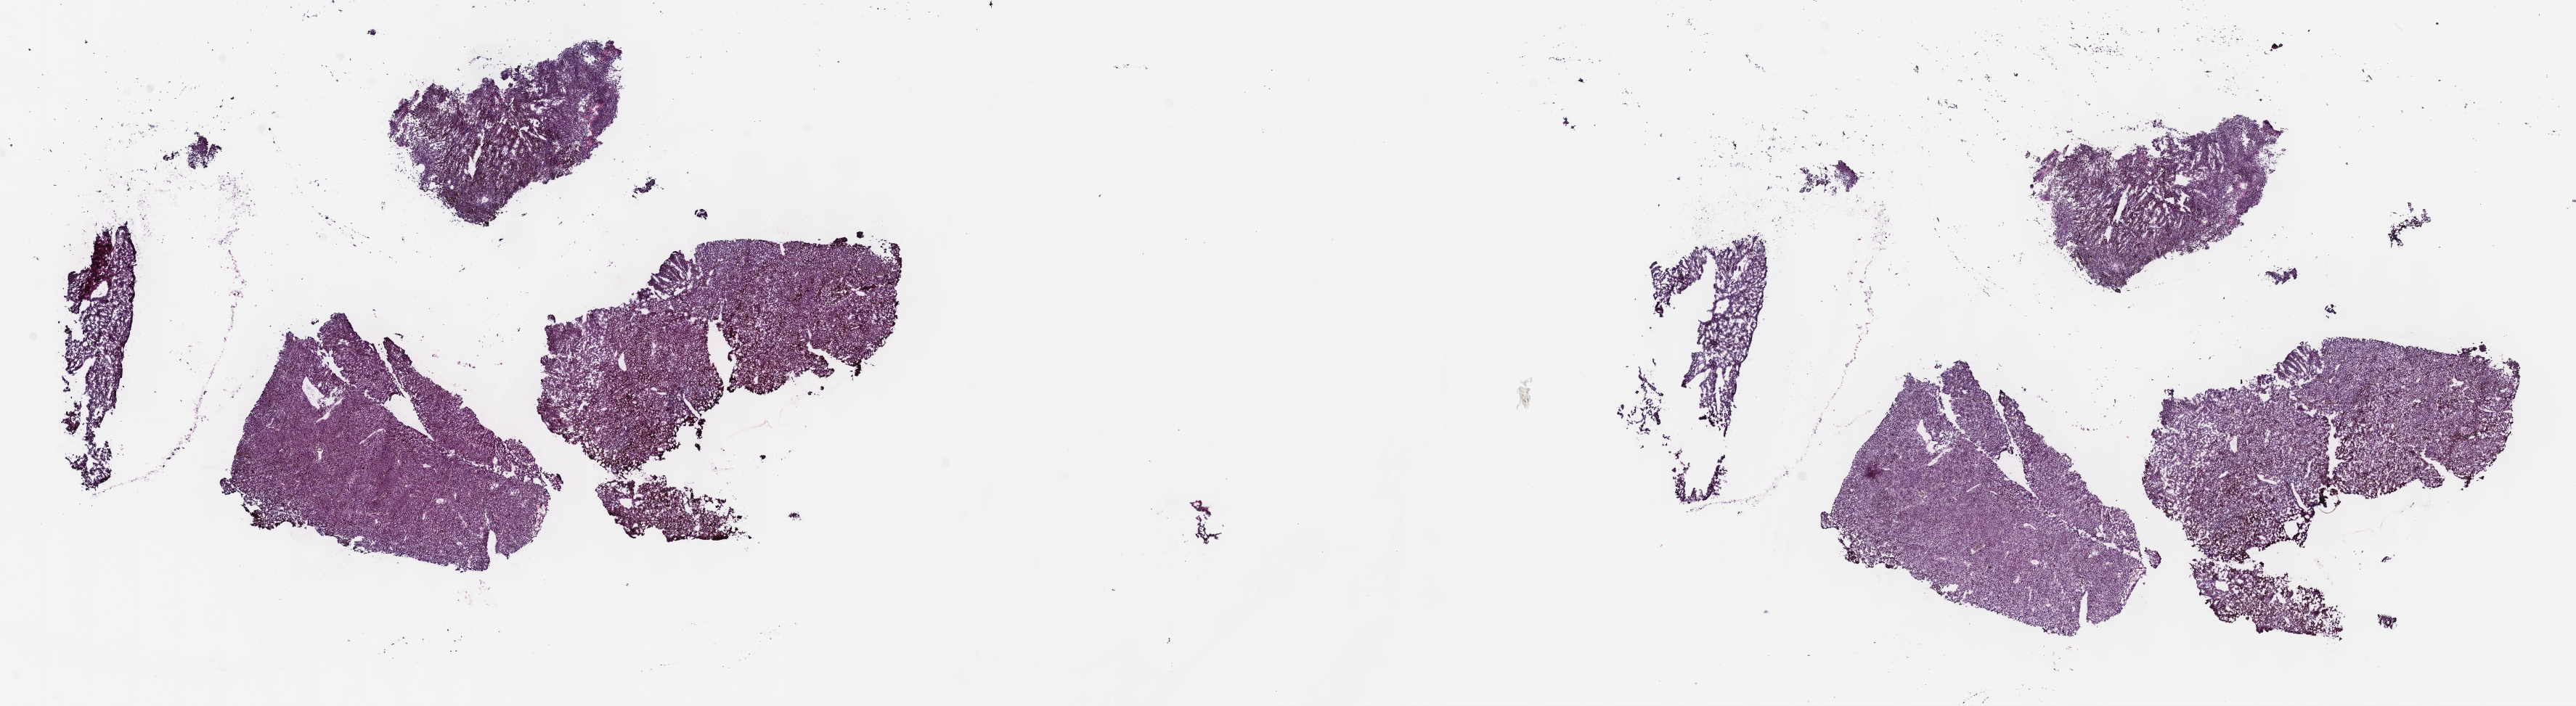
Whole-slide histology image, H&E-stained — a low-resolution overview of the entire scanned area, about 28.7 x 7.9 mm, frozen section from the top of the tissue portion, primary tumour sample from the uvea. Male patient; age at initial diagnosis 76 years. Composition of this section per pathologist review: tumour cells 80%, tumour nuclei 80%, normal cells 0%, stromal cells 20%, necrosis 0%. Inflammatory infiltration, as recorded: lymphocyte infiltration 3%, monocyte infiltration 2%, neutrophil infiltration 0%.
- AJCC pathologic stage: IIB (7th edition)
- pathologic diagnosis: Mixed epithelioid and spindle cell melanoma (choroid)
- laterality: right